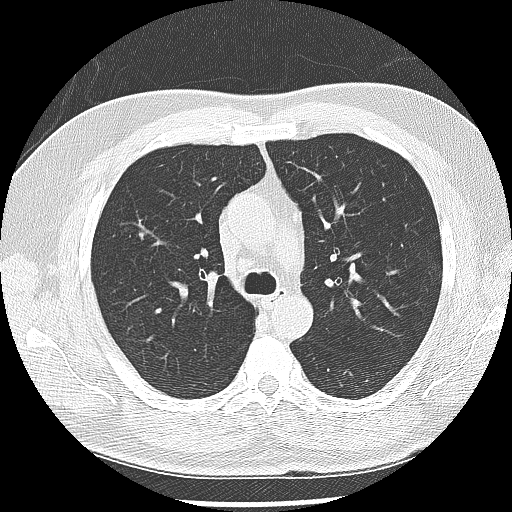
Low-dose screening chest CT, one axial slice. Position 180 of 265 along the scan axis. 120 kVp. Lung window (W 1500 / L -600 HU). 512 × 512 image matrix.
Outlined on this slice (expert manual segmentation):
- lesion 1 (tumor, upper lobe of right lung): box from (x=139, y=231) to (x=148, y=240) px